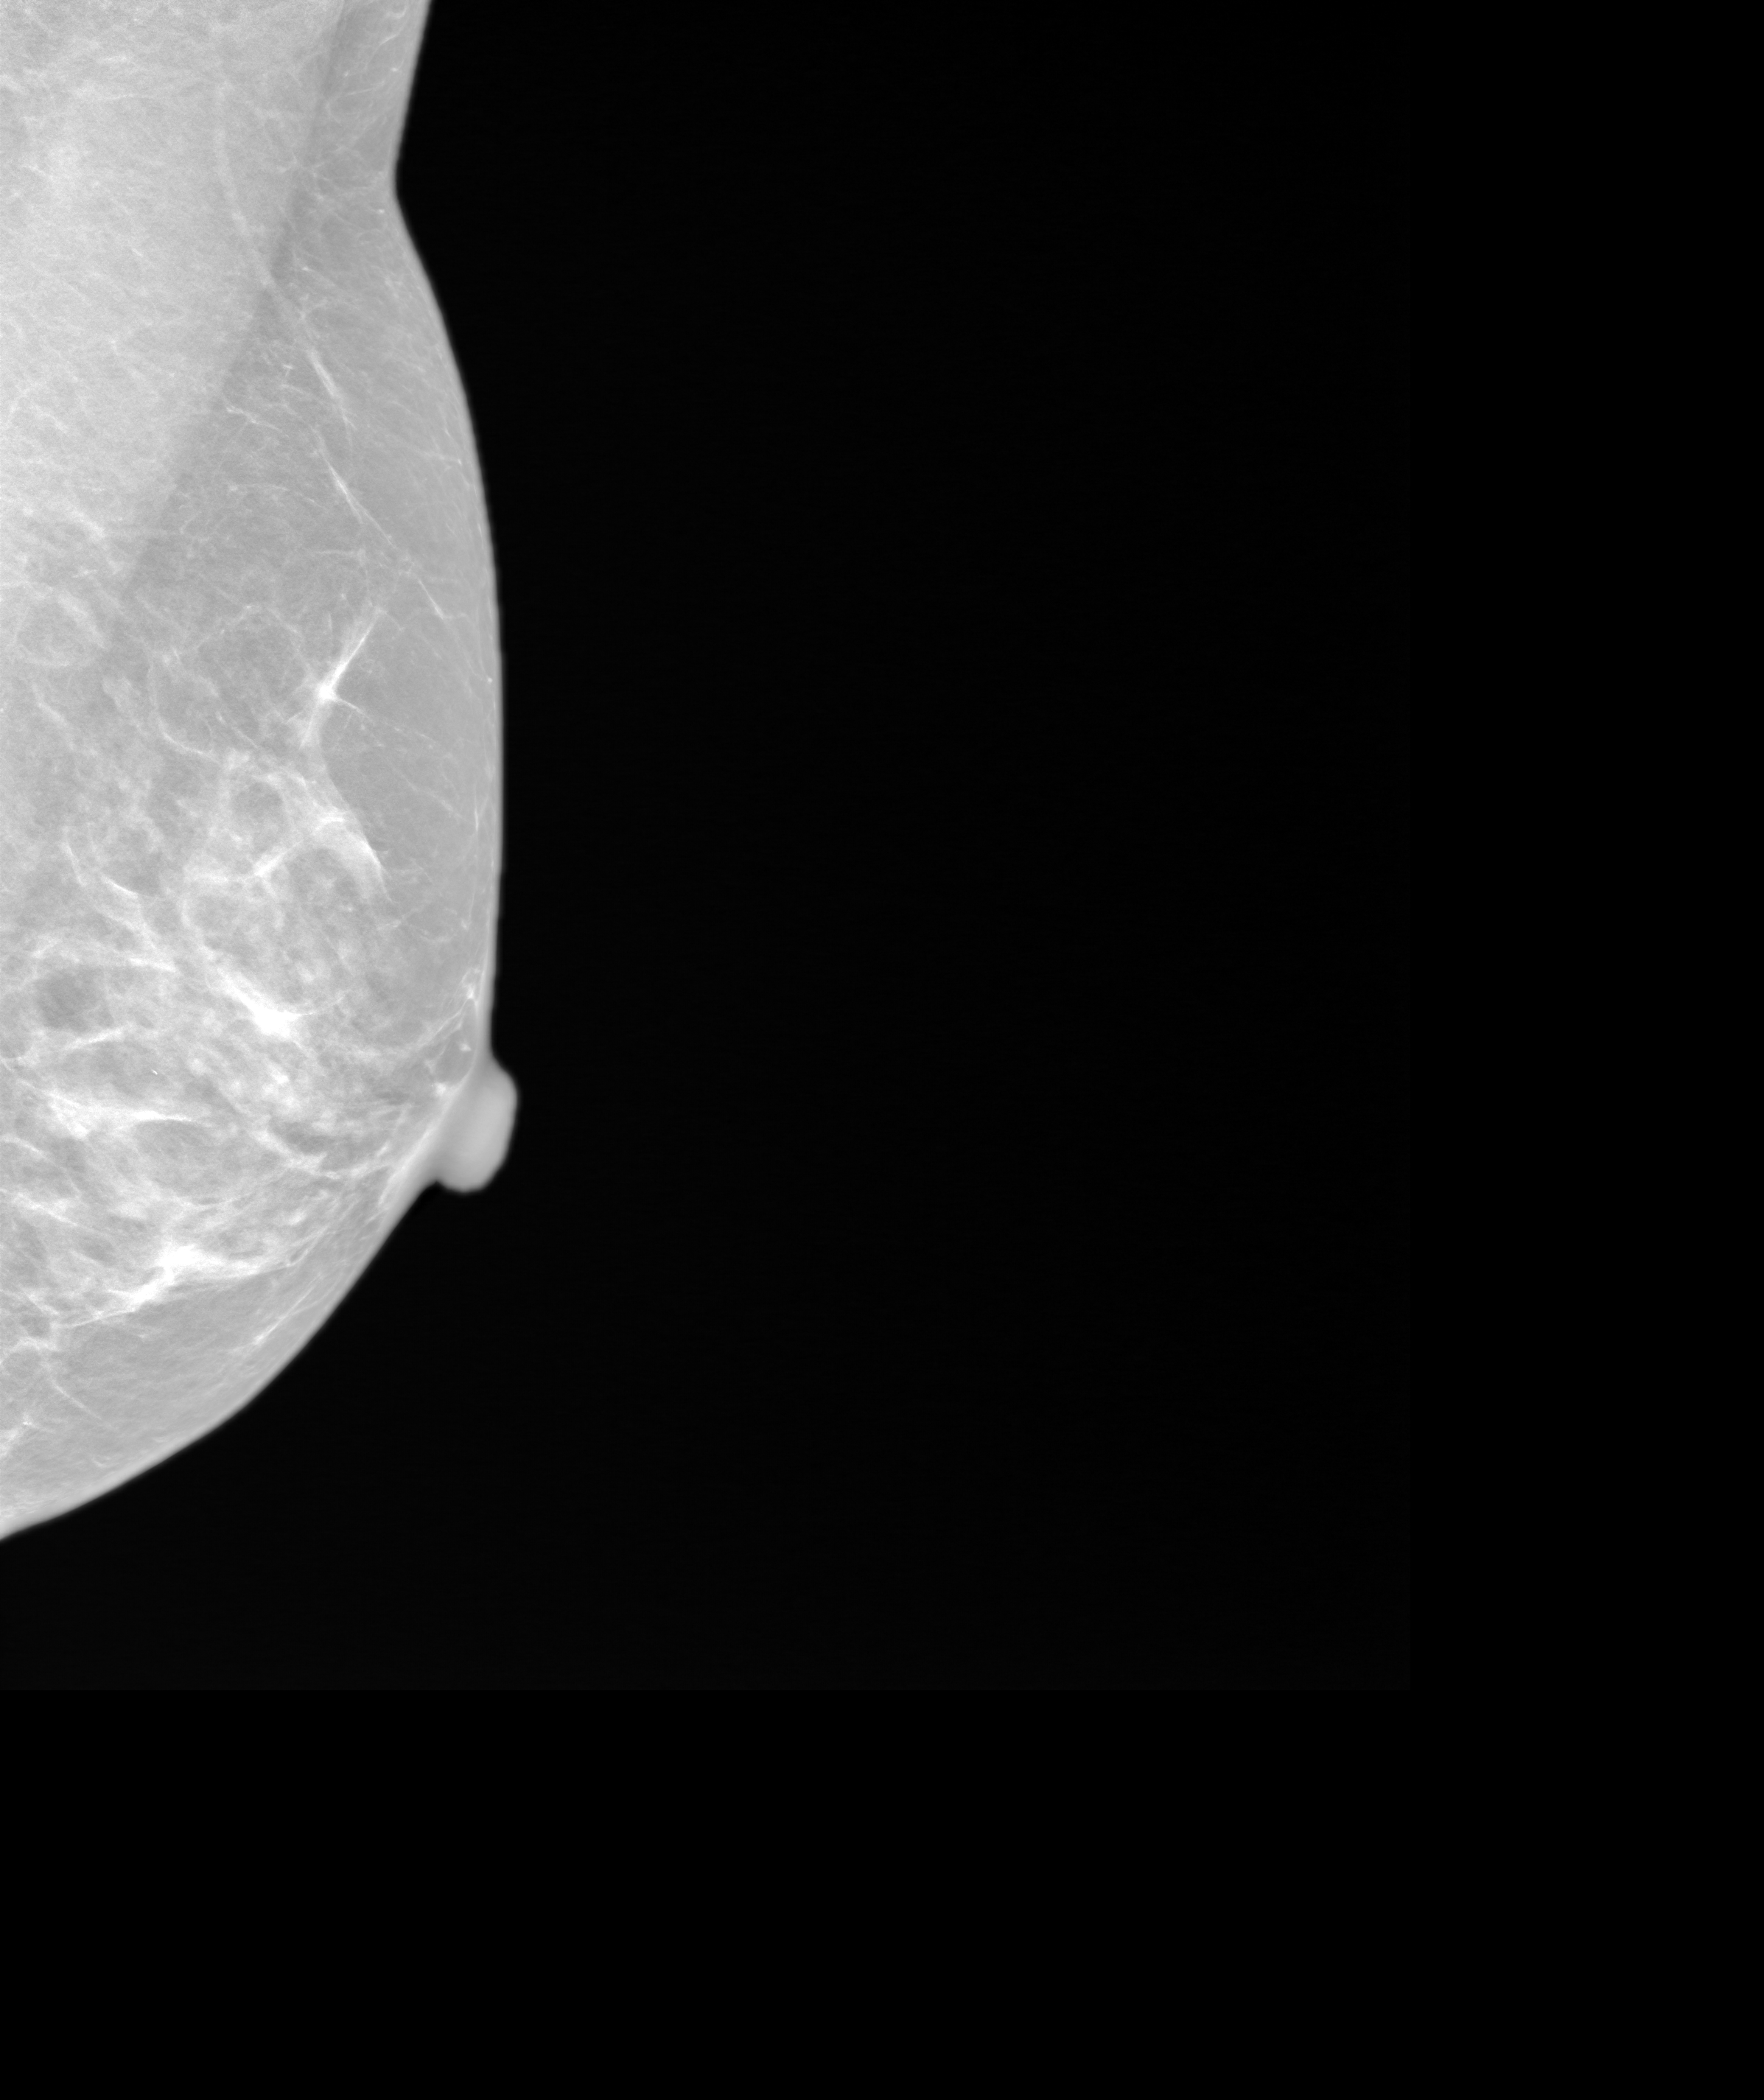
Screening examination. Patient aged 65 years (female).
Image type: synthesized 2-D view from tomosynthesis. Breast: left. Projection: medio-lateral oblique projection.